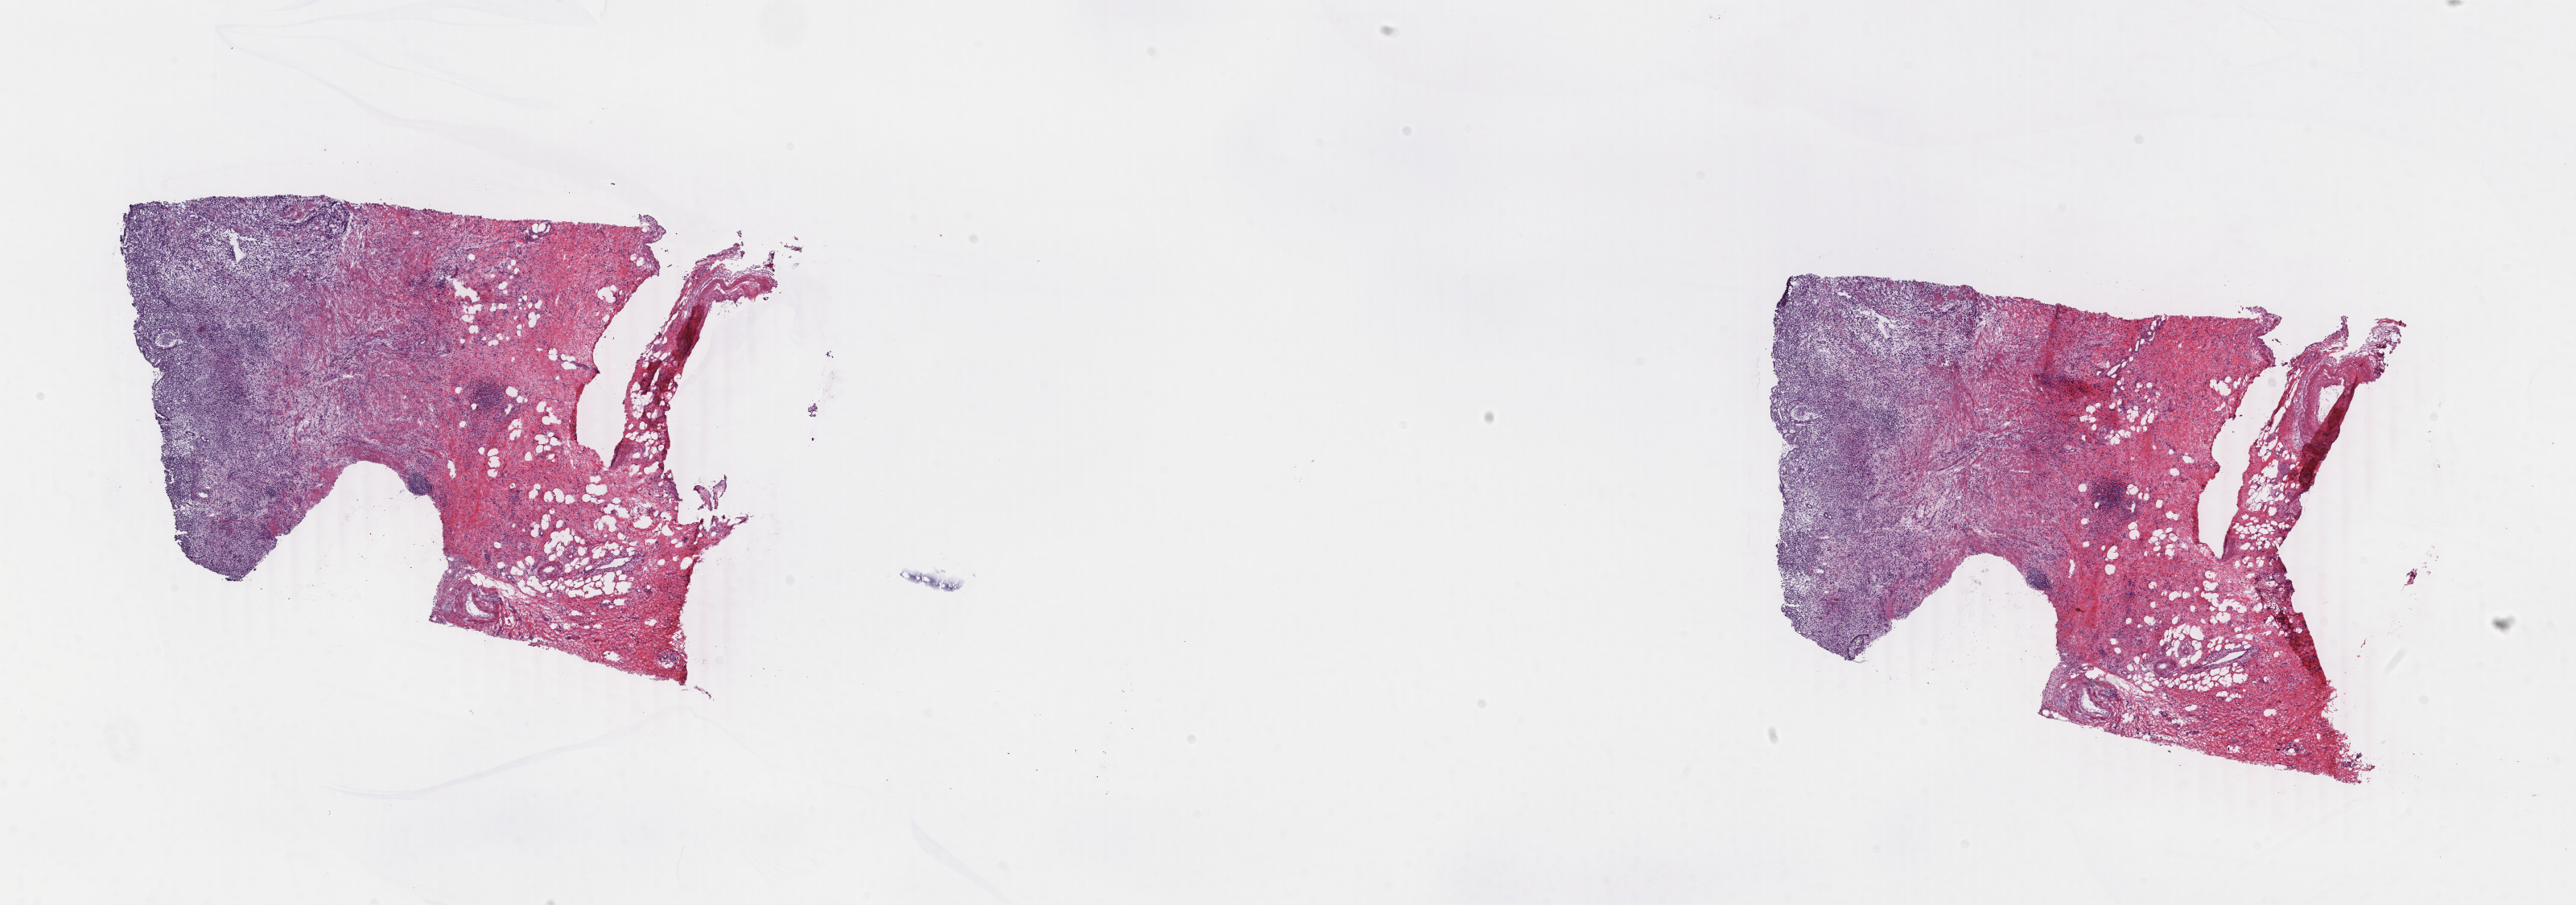
Whole-slide histology image, H&E, whole scanned area (about 25.5 x 8.9 mm, from a 40x scan) shown as a low-resolution overview; frozen section from the top of the tissue portion; primary tumour sample from the stomach. Patient: male, age at initial diagnosis 78 years. Histologic grade: G3 (poorly differentiated). Composition of this section per pathologist review: tumour cells 30%, tumour nuclei 60%, normal cells 0%, stromal cells 67%, necrosis 3%. Infiltration values recorded for this section: lymphocyte infiltration 10%, monocyte infiltration 3%, neutrophil infiltration 3%.
* histologic diagnosis: Carcinoma, diffuse type (gastric antrum)
* AJCC pathologic stage: IIIA